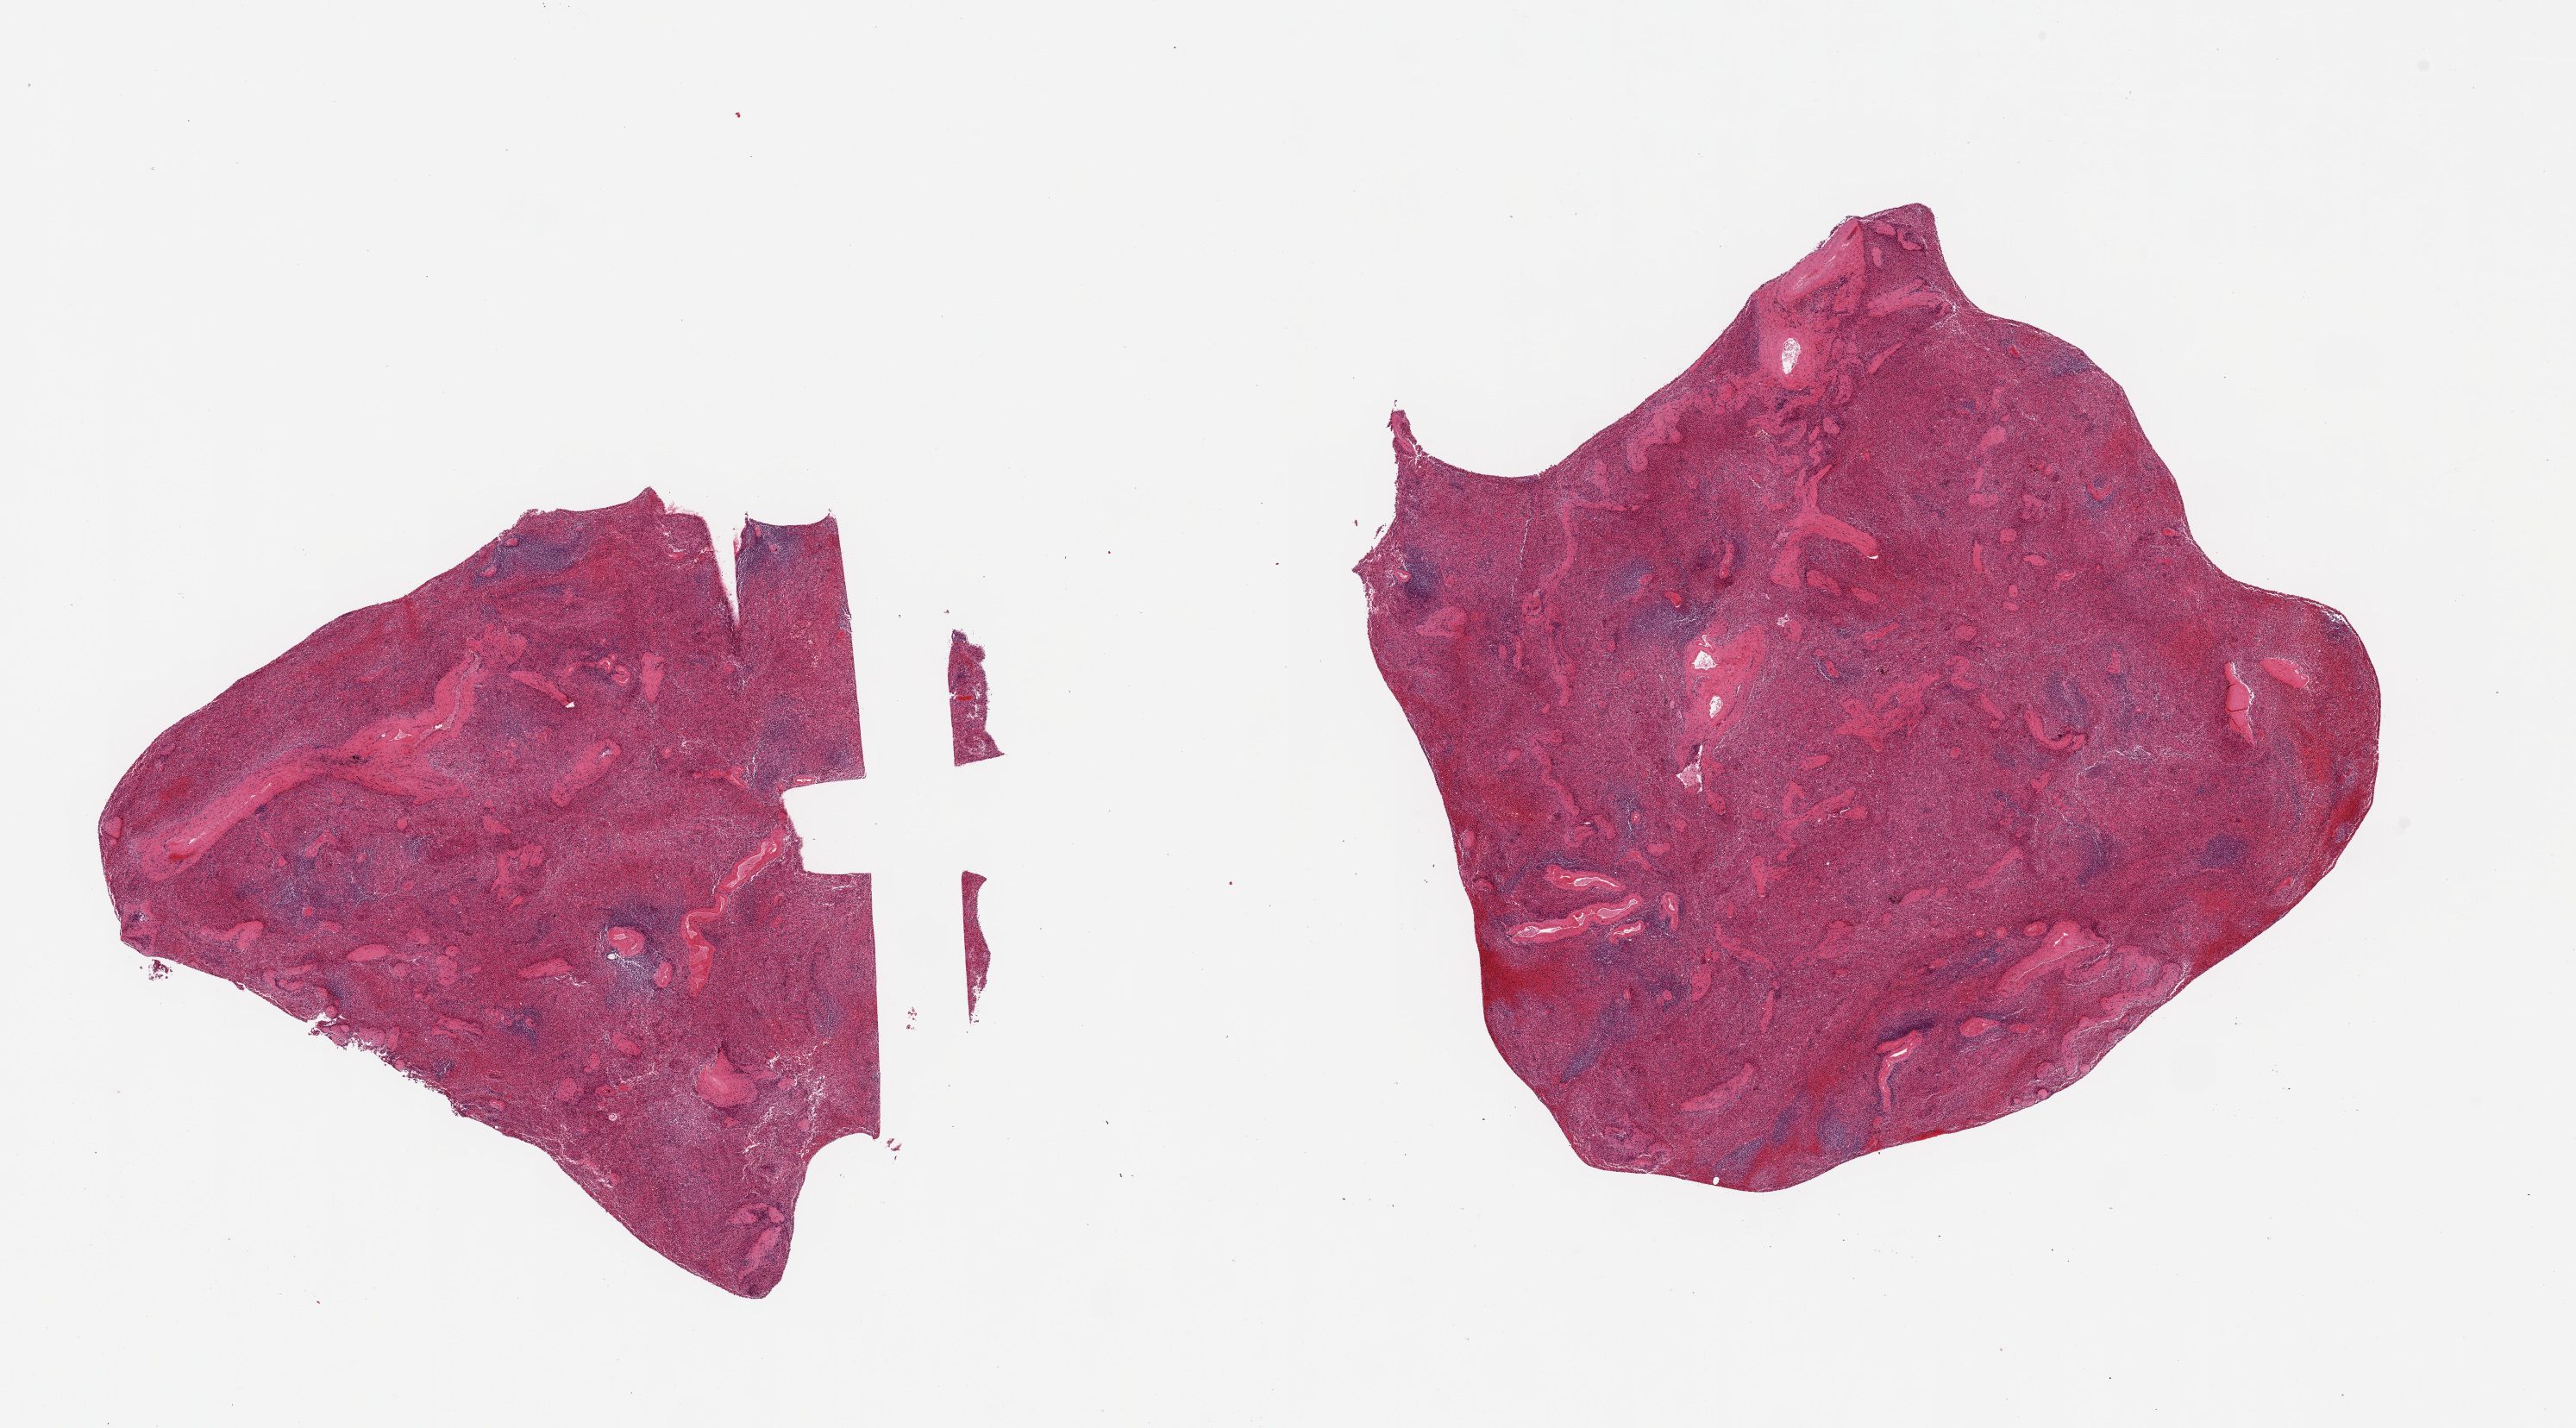
Digitized H&E-stained section, brightfield — a low-resolution overview of the entire scanned area, about 23.6 x 13.1 mm (from a 20x scan), PAXgene-fixed, paraffin-embedded tissue, sampled site (target tissue): spleen, donor tissue sample.
Reviewer comment on this tissue sample: 2 pieces, moderate/severe congestion.